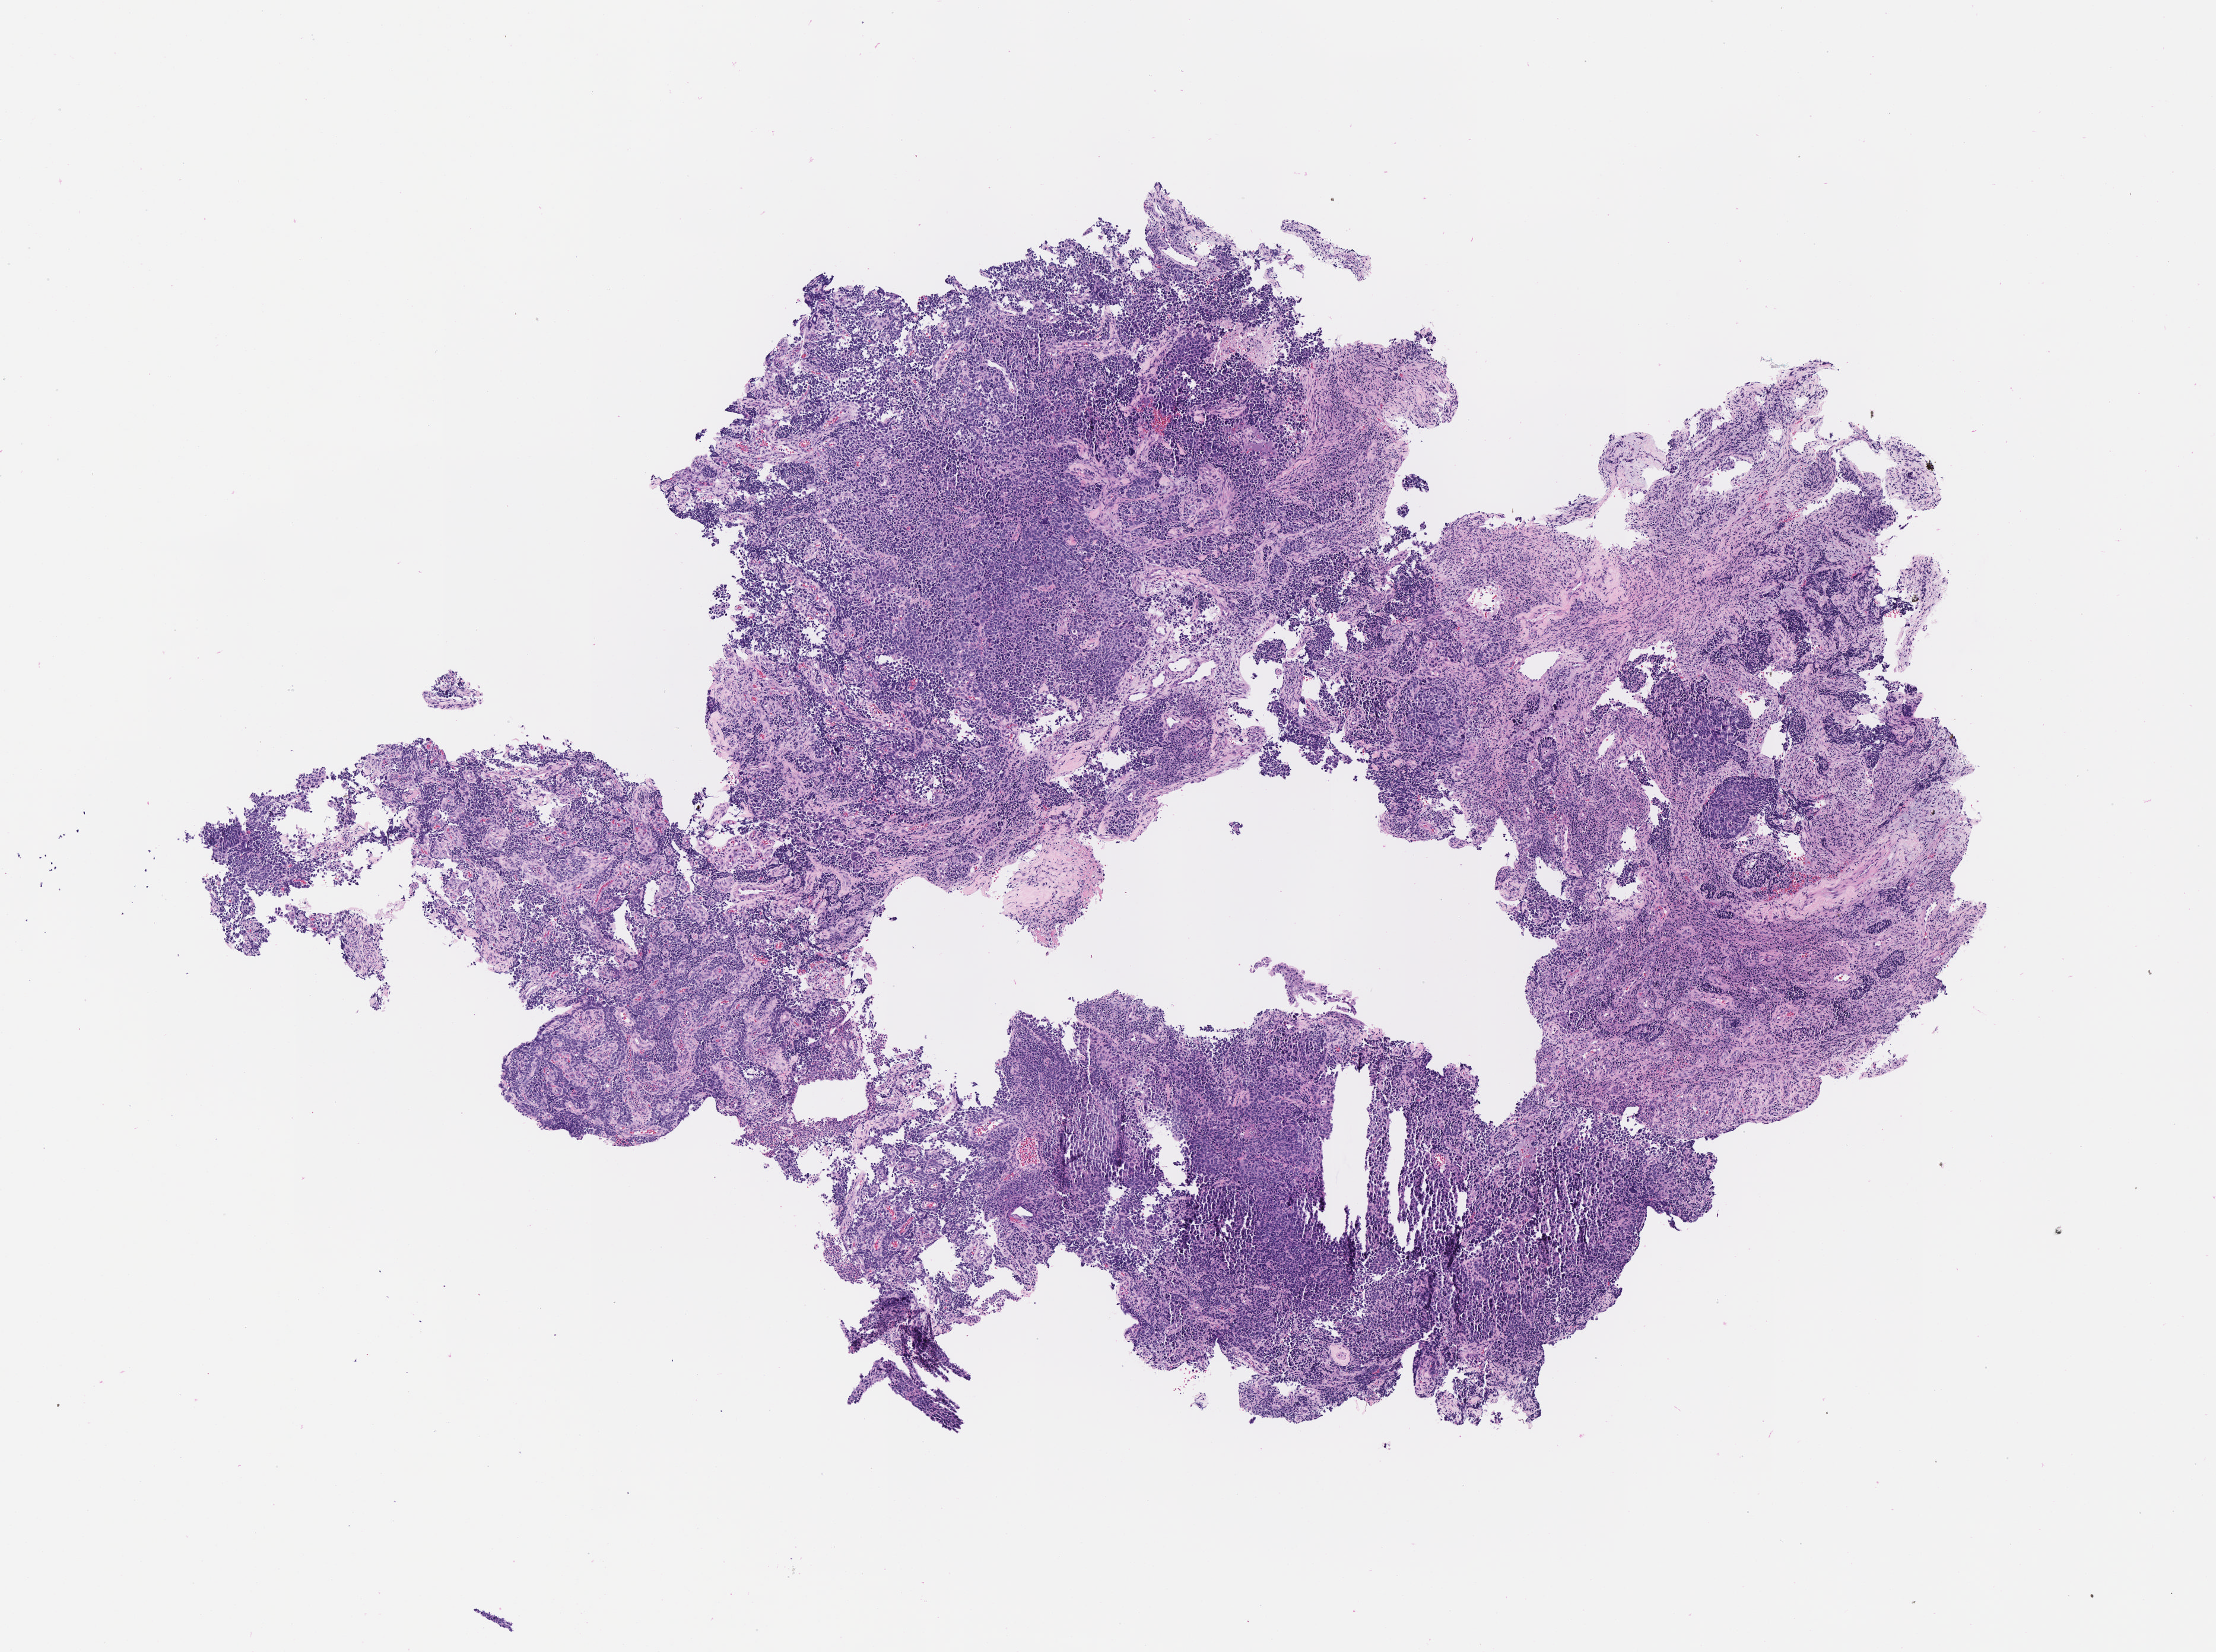
H&E whole-slide image, whole scanned area (about 7.5 x 5.6 mm) shown as a low-resolution overview. Tumor tissue. Site: cervix. Female patient, age 72 years.
Histologic diagnosis: Squamous cell carcinoma, large cell, nonkeratinizing, NOS.